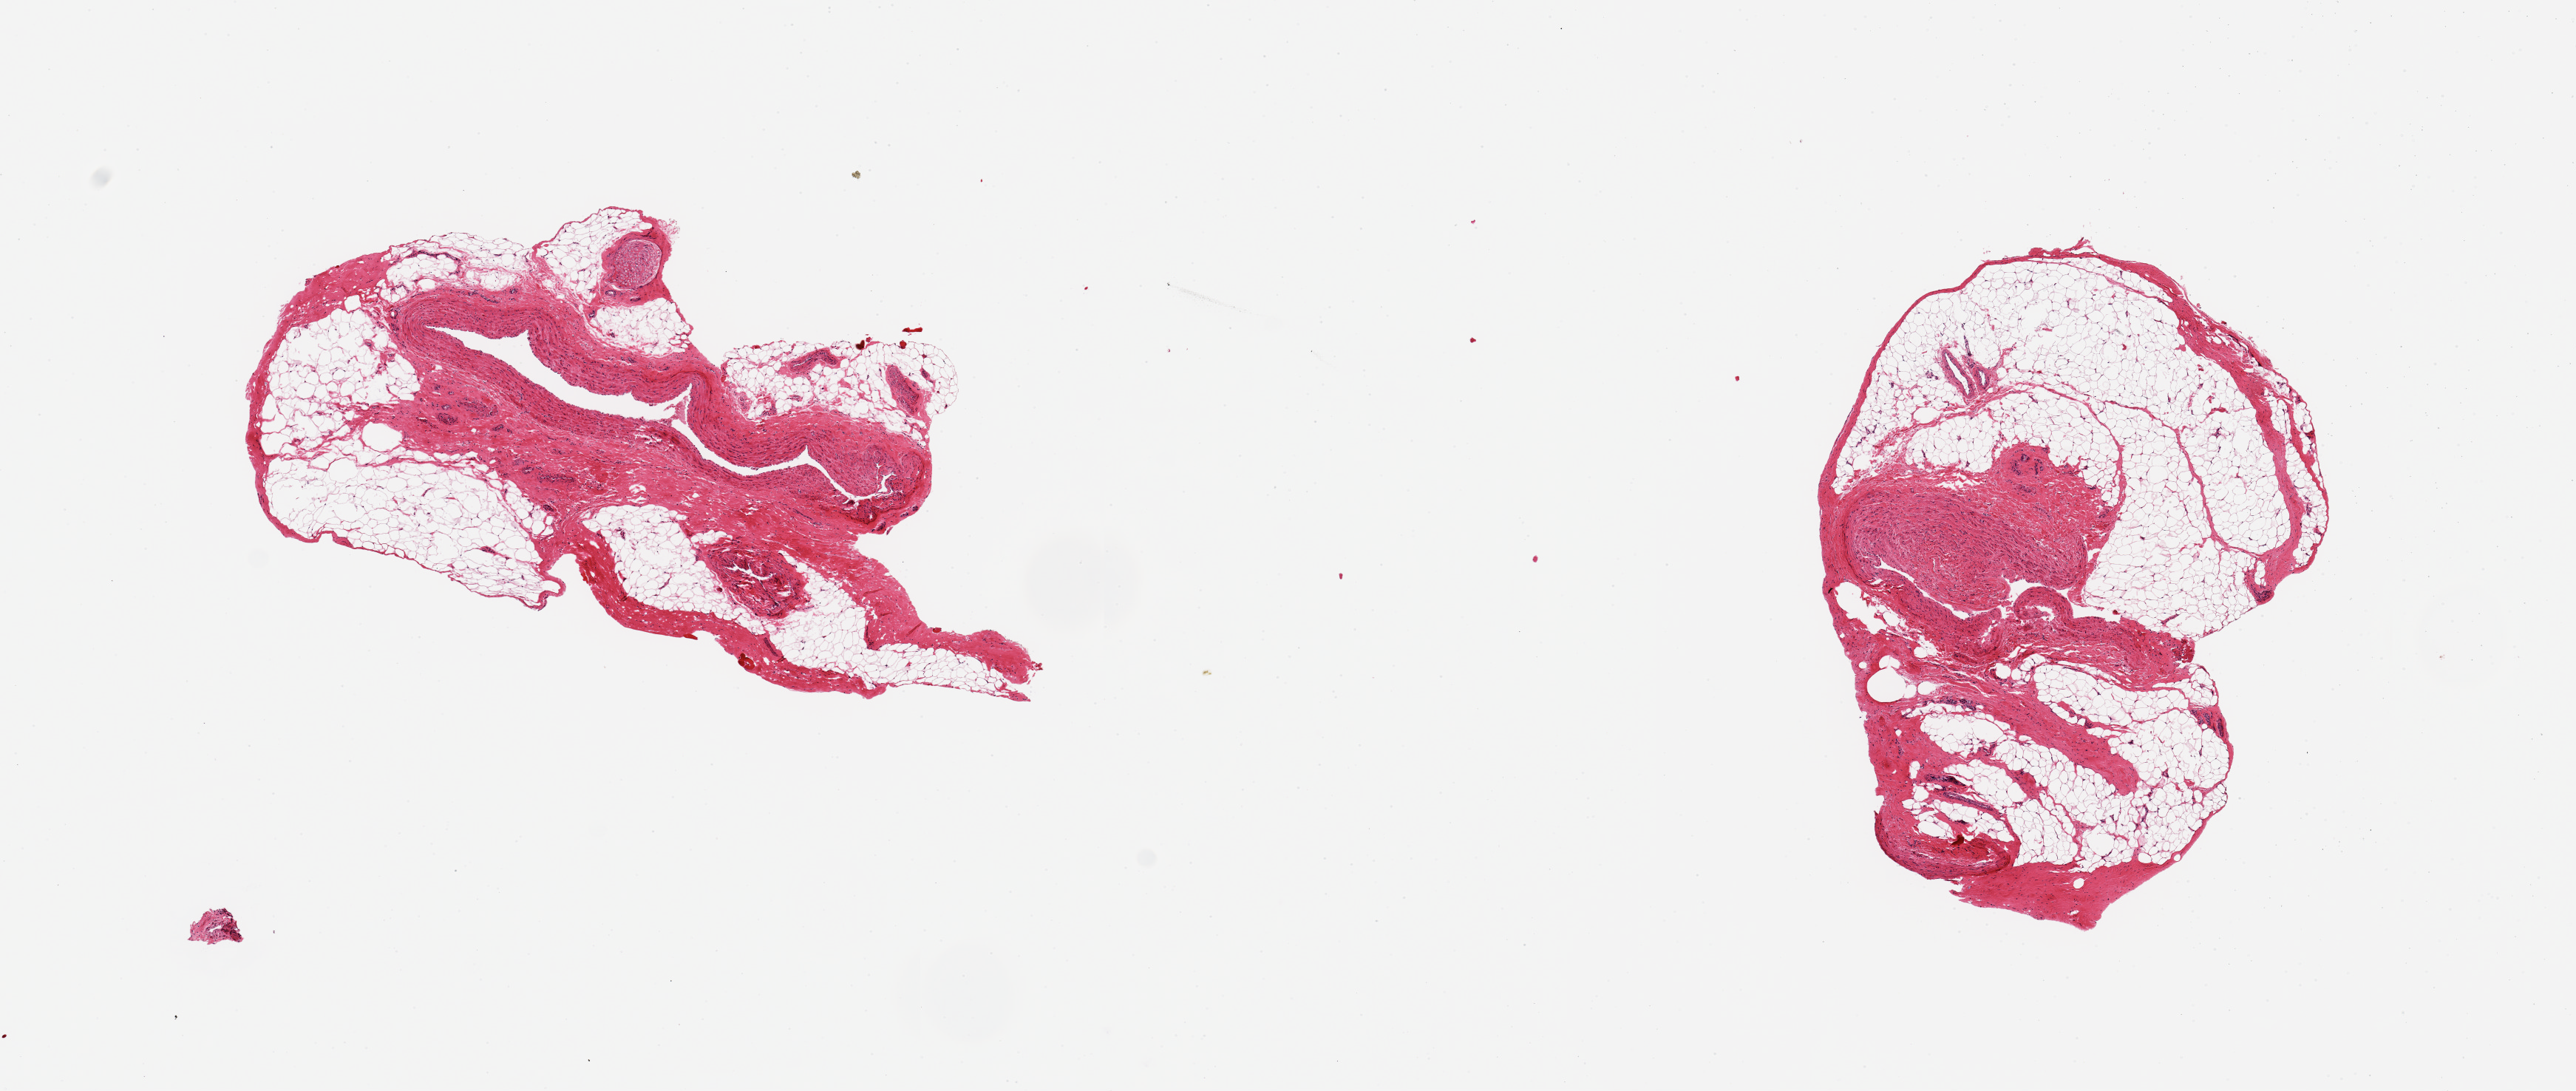
Hematoxylin and eosin (H&E) whole-slide image, low-resolution overview of the scanned area, about 13.8 x 5.8 mm (acquisition: 20x scan), PAXgene-fixed paraffin-embedded (PFPE) section, section of tibial artery (target tissue), tissue donor sample. Donor: male.
Review note (as recorded): 2 pieces, 4x2 & 3x3 mm; ~60% adipose surrounds vessels.